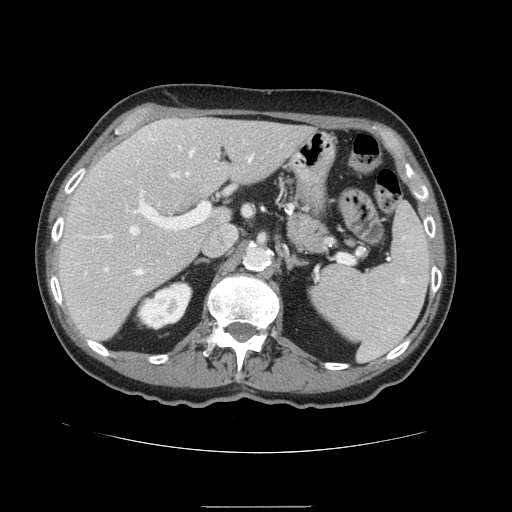
Contrast-enhanced abdominal CT, one axial slice; slice 94 of 168 in the series (ordered by position); 120 kVp; soft-tissue window (W 400 / L 40 HU); 512 × 512 image matrix, field of view 386 × 386 mm. Male patient, age 74 years. Case-level facts recorded for this patient, not image findings: diagnosis: colorectal cancer liver metastases, imaged before liver resection; multiple liver metastases: no; largest metastasis: 14.5 cm.
Annotated regions visible in this slice (outlined manually by an expert reader):
- hepatic veins: bounding box <130,151,253,273> (left, top, right, bottom; pixels)
- liver: <58,119,315,342>
- planned liver remnant (the part of the liver to remain after resection): <58,119,315,342>
- portal vein (with intrahepatic branches): <78,194,210,271>